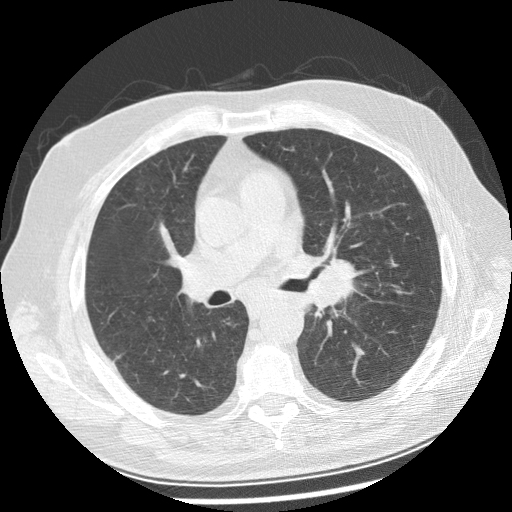
Low-dose screening chest CT, axial slice. Baseline annual screen. Lung window (W 1500 / L -600 HU). 2.5 mm slice thickness. Male participant, aged 70 years at enrolment. Current smoker at enrolment.
Expert reader's lesion annotation, bounding box (x1, y1, x2, y2) in pixels: (284, 242, 366, 313). Screening reader's record for this exam: no non-calcified nodule ≥4 mm recorded. Lung cancer was diagnosed 29 days after this screen: squamous cell carcinoma, keratinizing, NOS, left main stem bronchus, moderately differentiated (G2), stage IIIB (AJCC 6th edition), 40 mm at pathology.